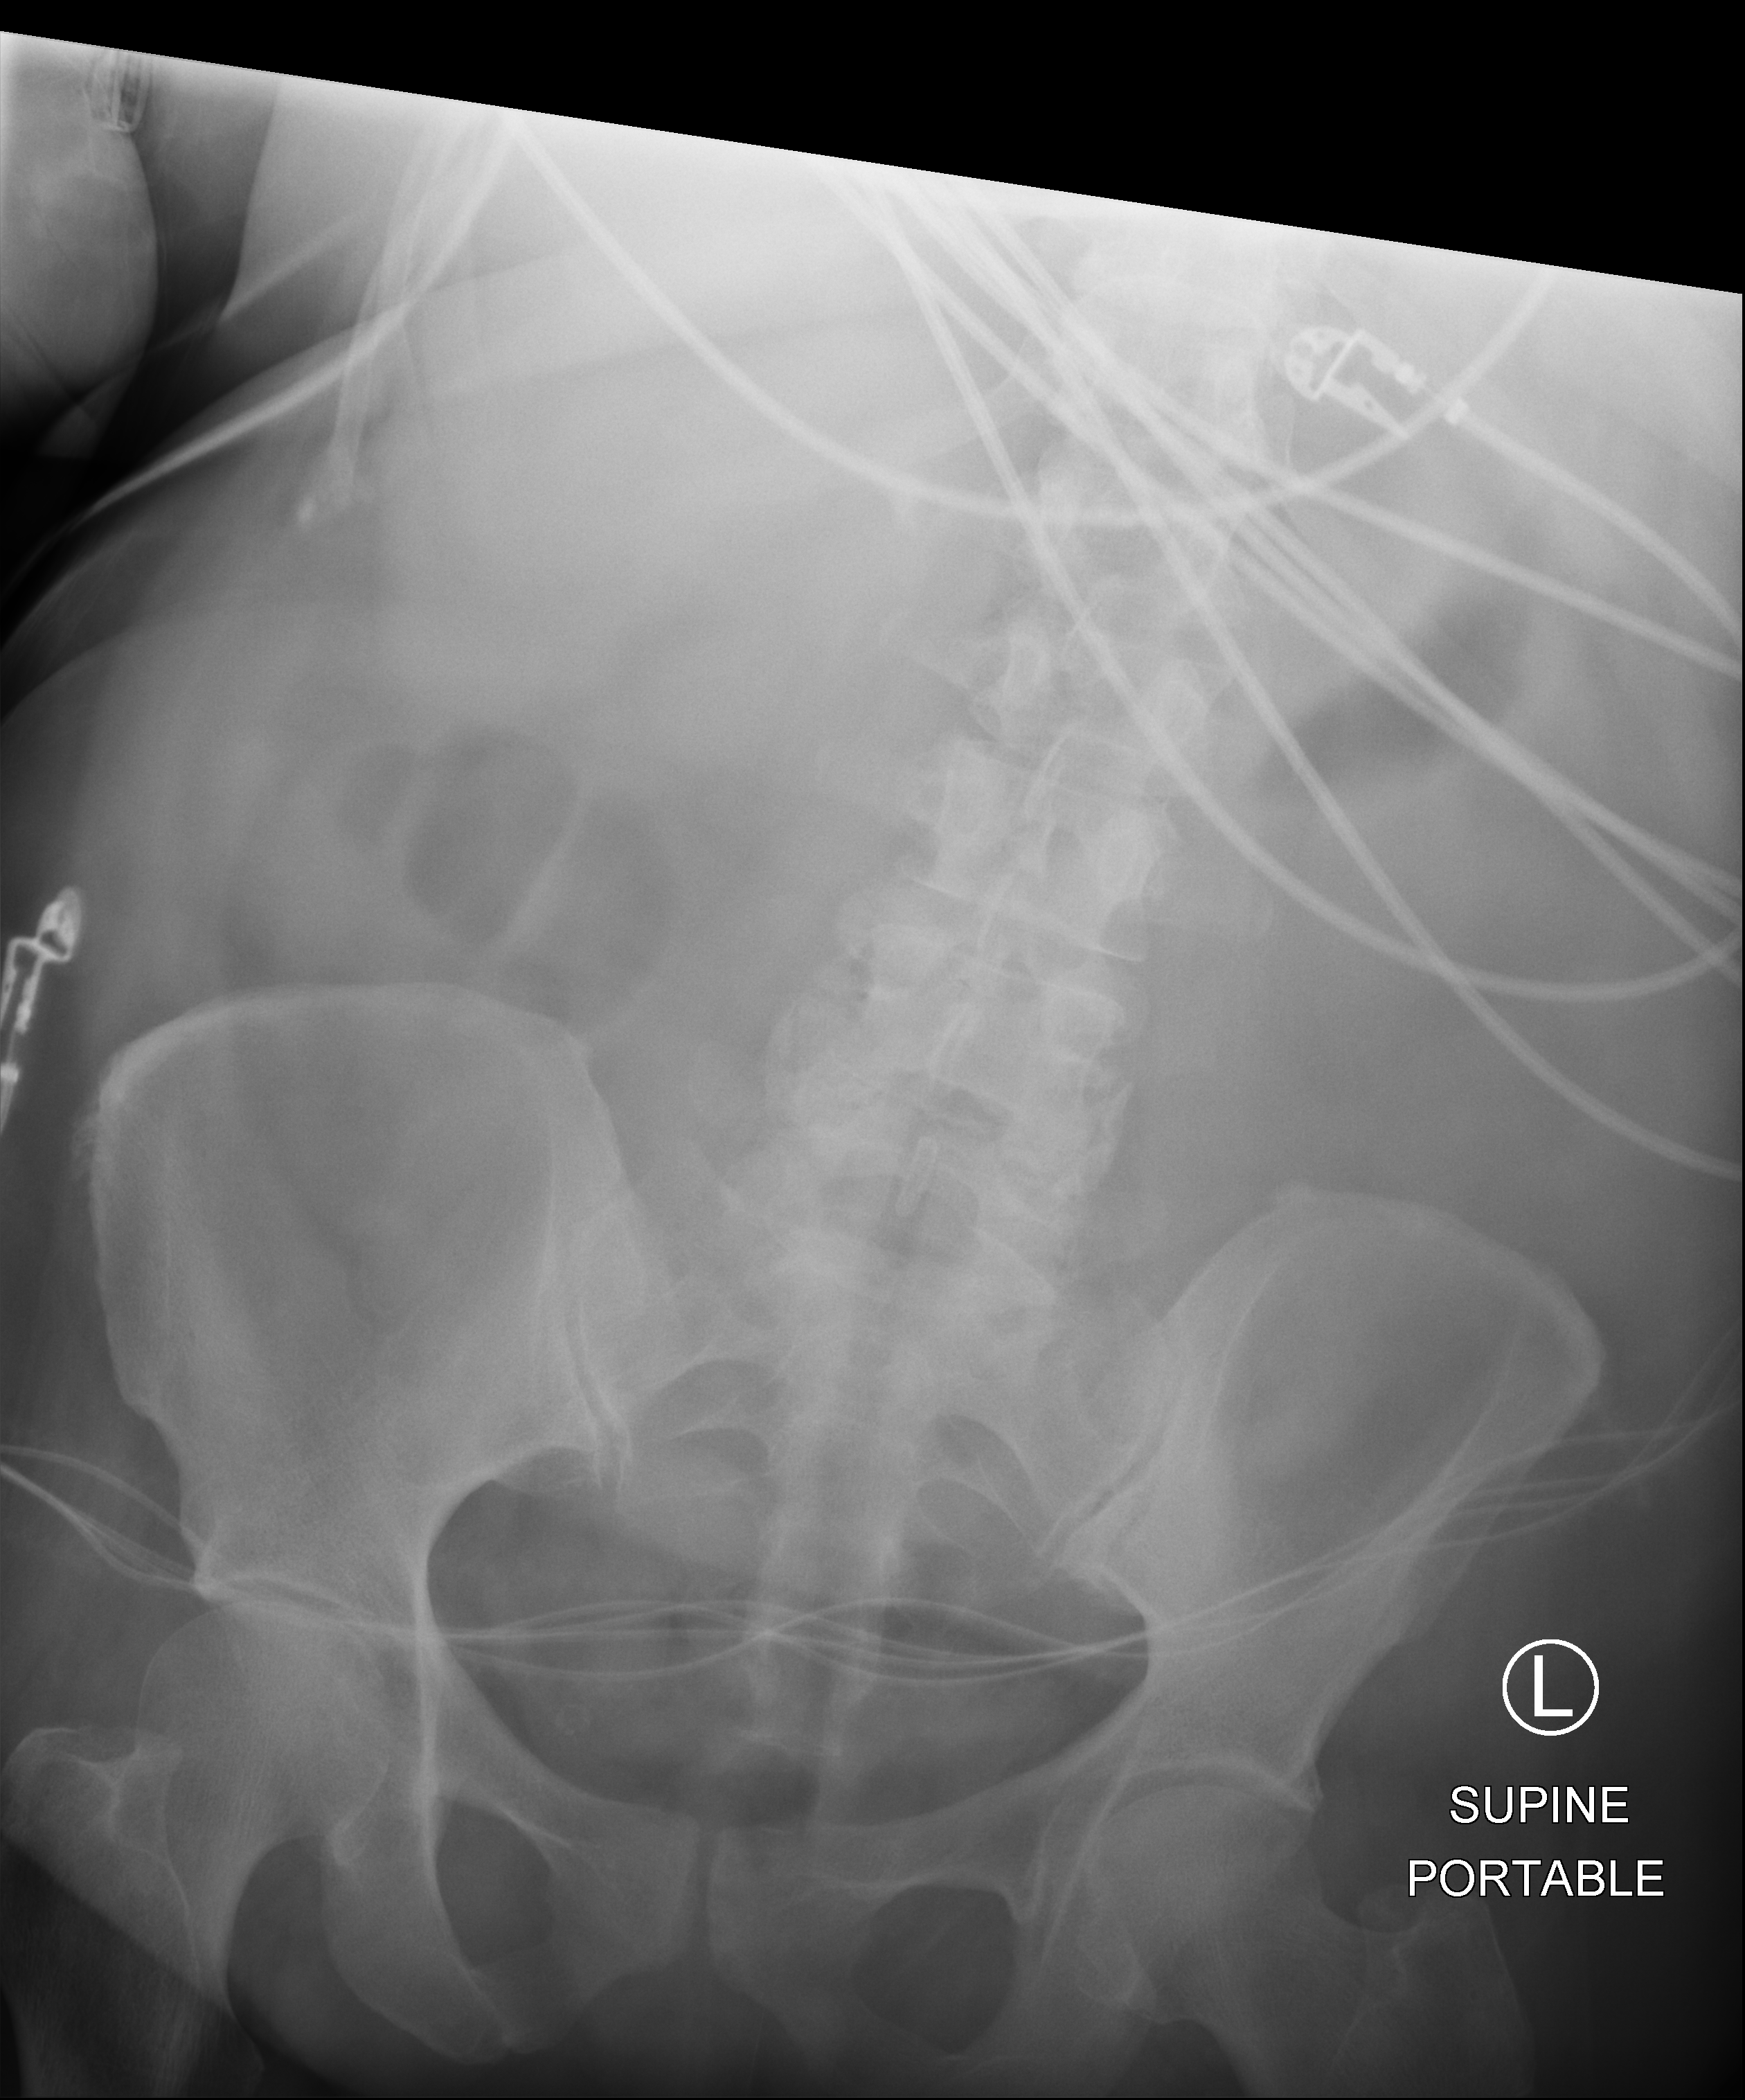
Abdomen X-ray (portable). Patient hospitalised with COVID-19; female, aged 60–74 years.
Hospital-stay facts (about this admission, not read from this image; timing relative to this image not recorded):
- chronic kidney disease (admission record): no
- other chronic lung disease (admission record): yes
- admitted to intensive care during this hospital stay: yes